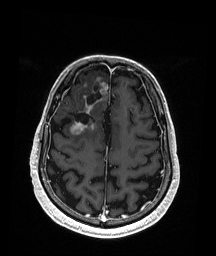
Brain MRI from a brain-tumour surgery series, one axial slice. Slice 57 of 192 in the series (ordered by position). T1-weighted post-contrast. 1 mm slice thickness. 216 × 256 image matrix. From the clinical record (not read from this slice): histopathology: Astrocytoma; WHO grade: 3; IDH mutation: yes.
Structures marked on this image (outlined manually by an expert reader):
- previous resection cavity: bounding box [x1, y1, x2, y2] px = [68, 87, 101, 124]
- tumour: [70, 83, 109, 136]